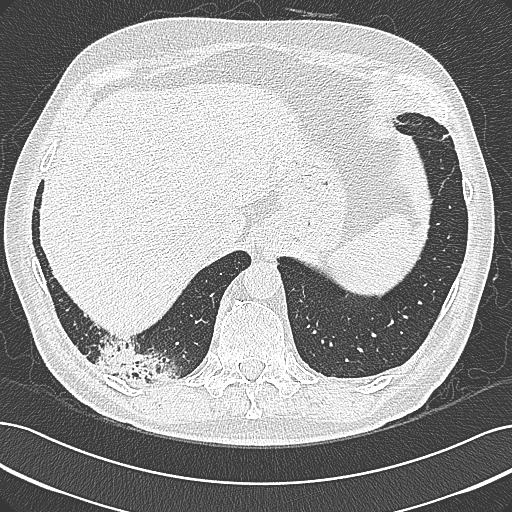
Chest CT (low-dose screening protocol), one axial image. Baseline annual screen. Lung window (W 1500 / L -600 HU). 1 mm slice thickness. Lung (sharp) reconstruction kernel (B80f). Male, age 68 years at enrolment. Former smoker at enrolment.
- Expert-annotated lung lesion, bounding box [x1, y1, x2, y2] px = [94, 337, 192, 398].
- Screening reader's record for this exam: no non-calcified nodule ≥4 mm recorded.
- Official screen result: negative screen, significant abnormalities not suspicious for lung cancer.
- Participant outcome: lung cancer diagnosed 154 days after this screen — mucinous adenocarcinoma, right lower lobe, well differentiated (G1), stage IB (AJCC 6th edition), 50 mm at pathology.